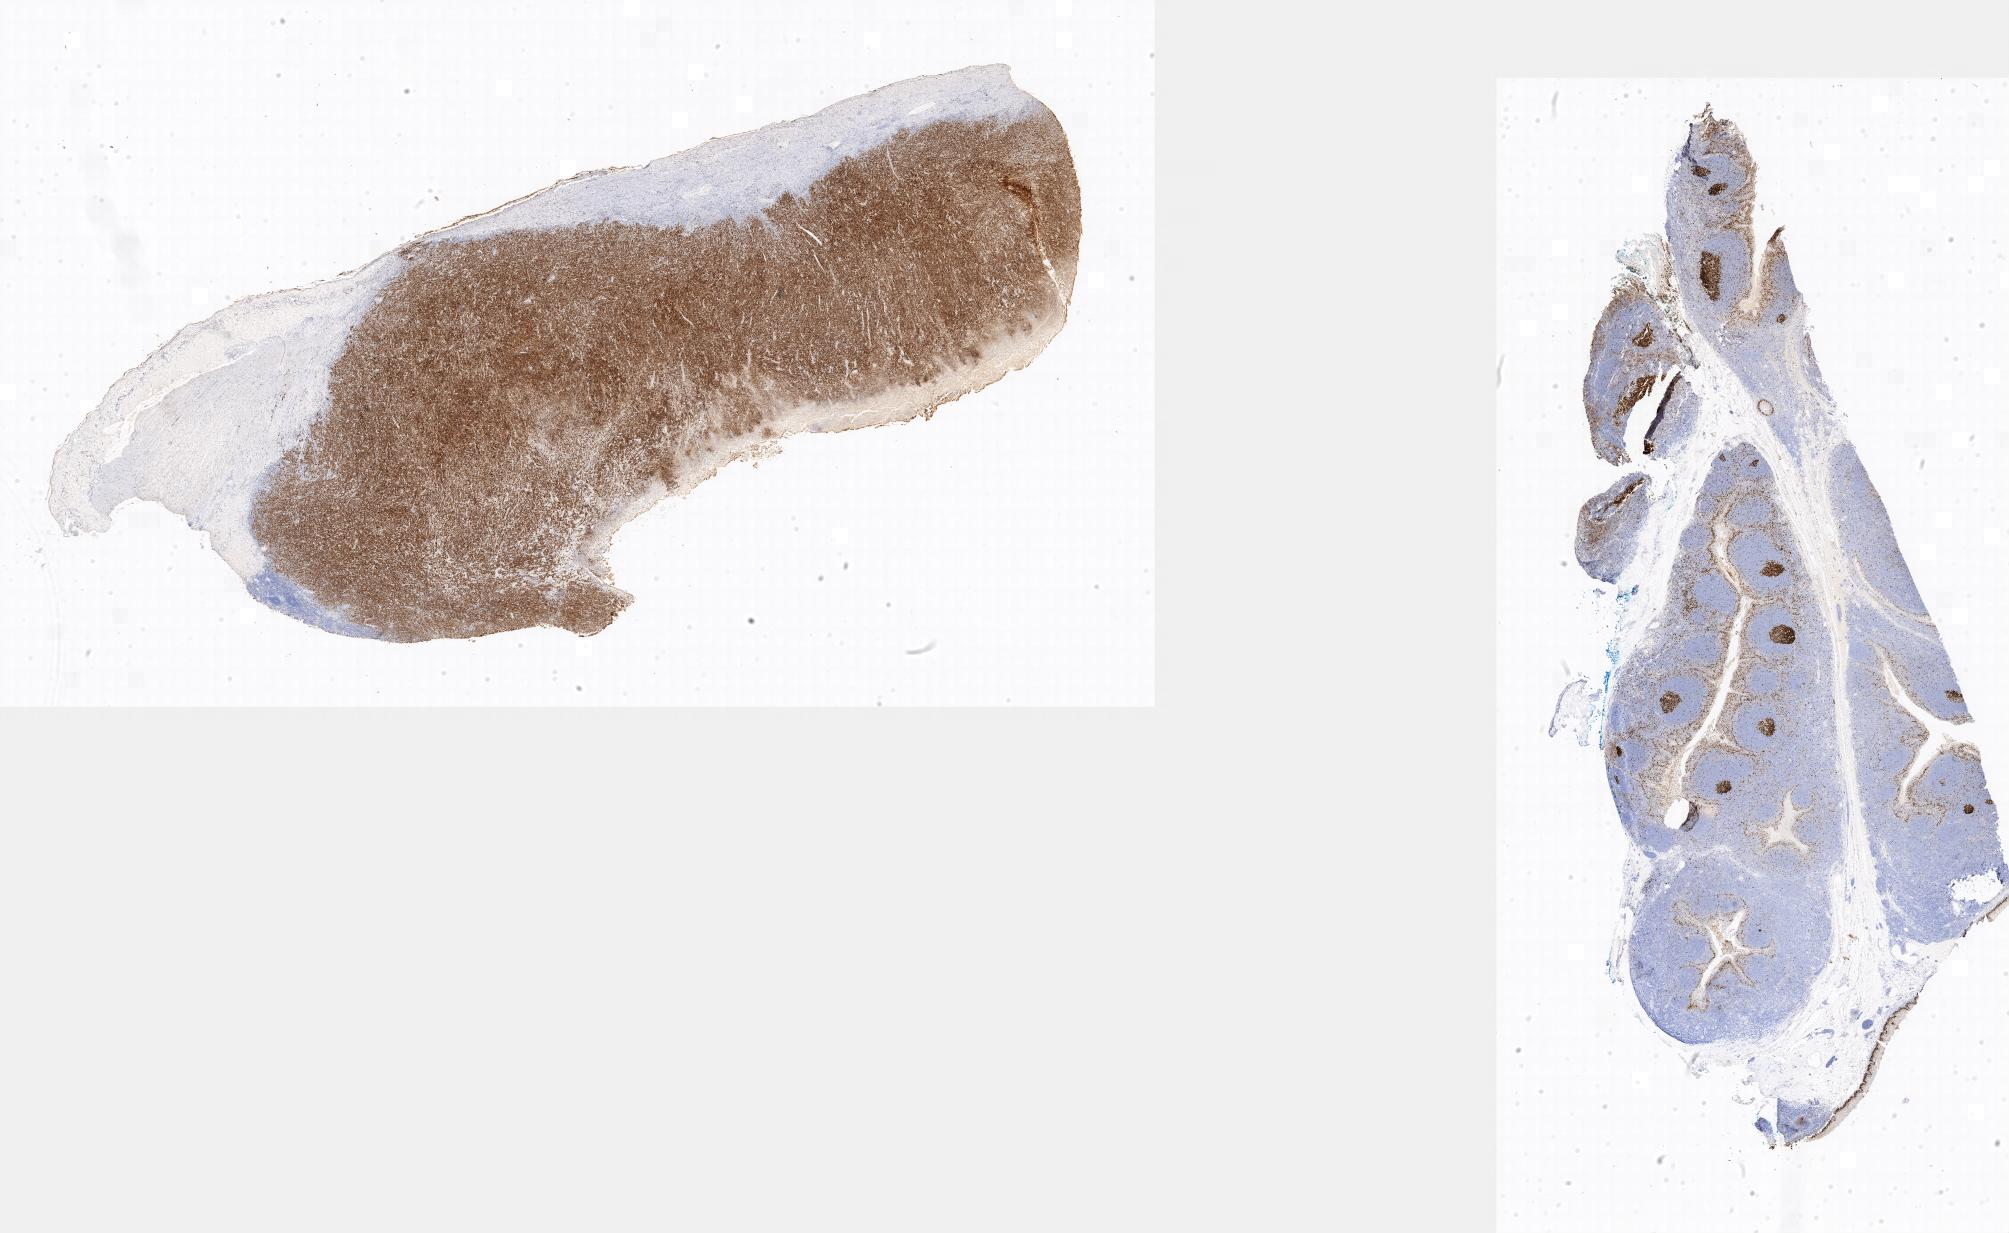
Immunohistochemistry (IHC) whole-slide image stained for Ki-67, shown as a low-resolution overview of the whole scanned area. Tumor tissue. Anatomic site: small intestine. Male, age 3 years at initial diagnosis.
Diagnosis: Burkitt lymphoma, NOS.